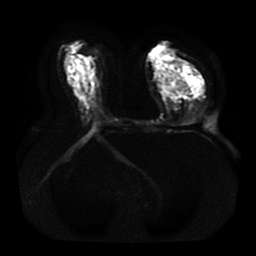
Breast MRI, one axial slice; position 24 of 41 along the scan axis; diffusion-weighted series; image 2 of 4 stored at this slice position (different b-values; order by instance number); 1.5 T; 5 mm slice thickness; 256 × 256 image matrix, field of view 330 × 330 mm. Female patient.
Structures marked on this image (manually delineated by an expert):
- tumour on diffusion-weighted imaging: bounding box <162,65,204,94> (left, top, right, bottom; pixels)